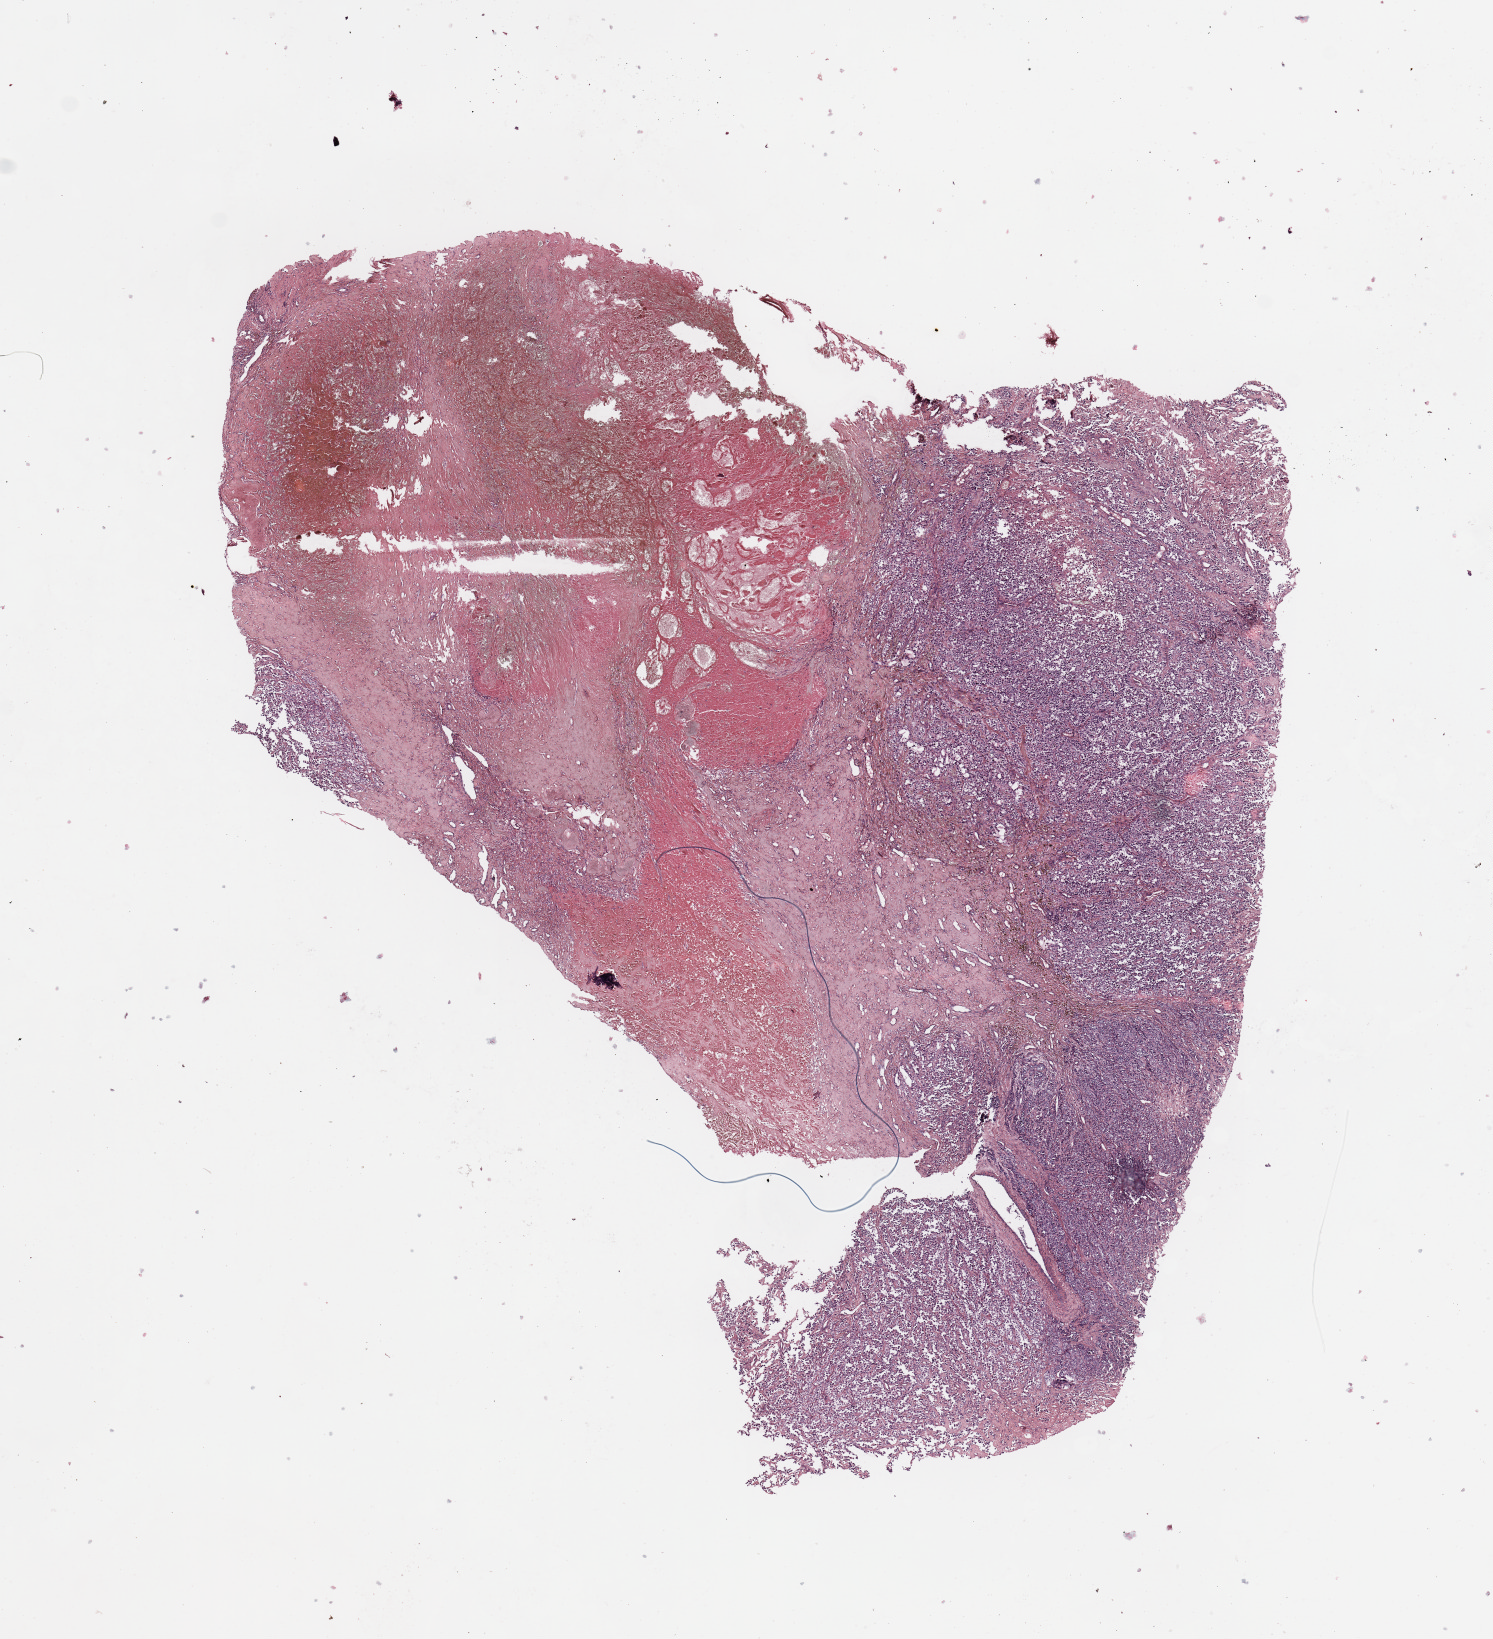
Whole-slide histology image, H&E, low-resolution overview of the scanned area, about 11.8 x 13.0 mm, melanoma tumour tissue; sampled site not recorded. 80-year-old female patient.
Diagnosis: Malignant melanoma, NOS. Primary tumour site (as recorded): trunk. AJCC pathologic stage: IIA.